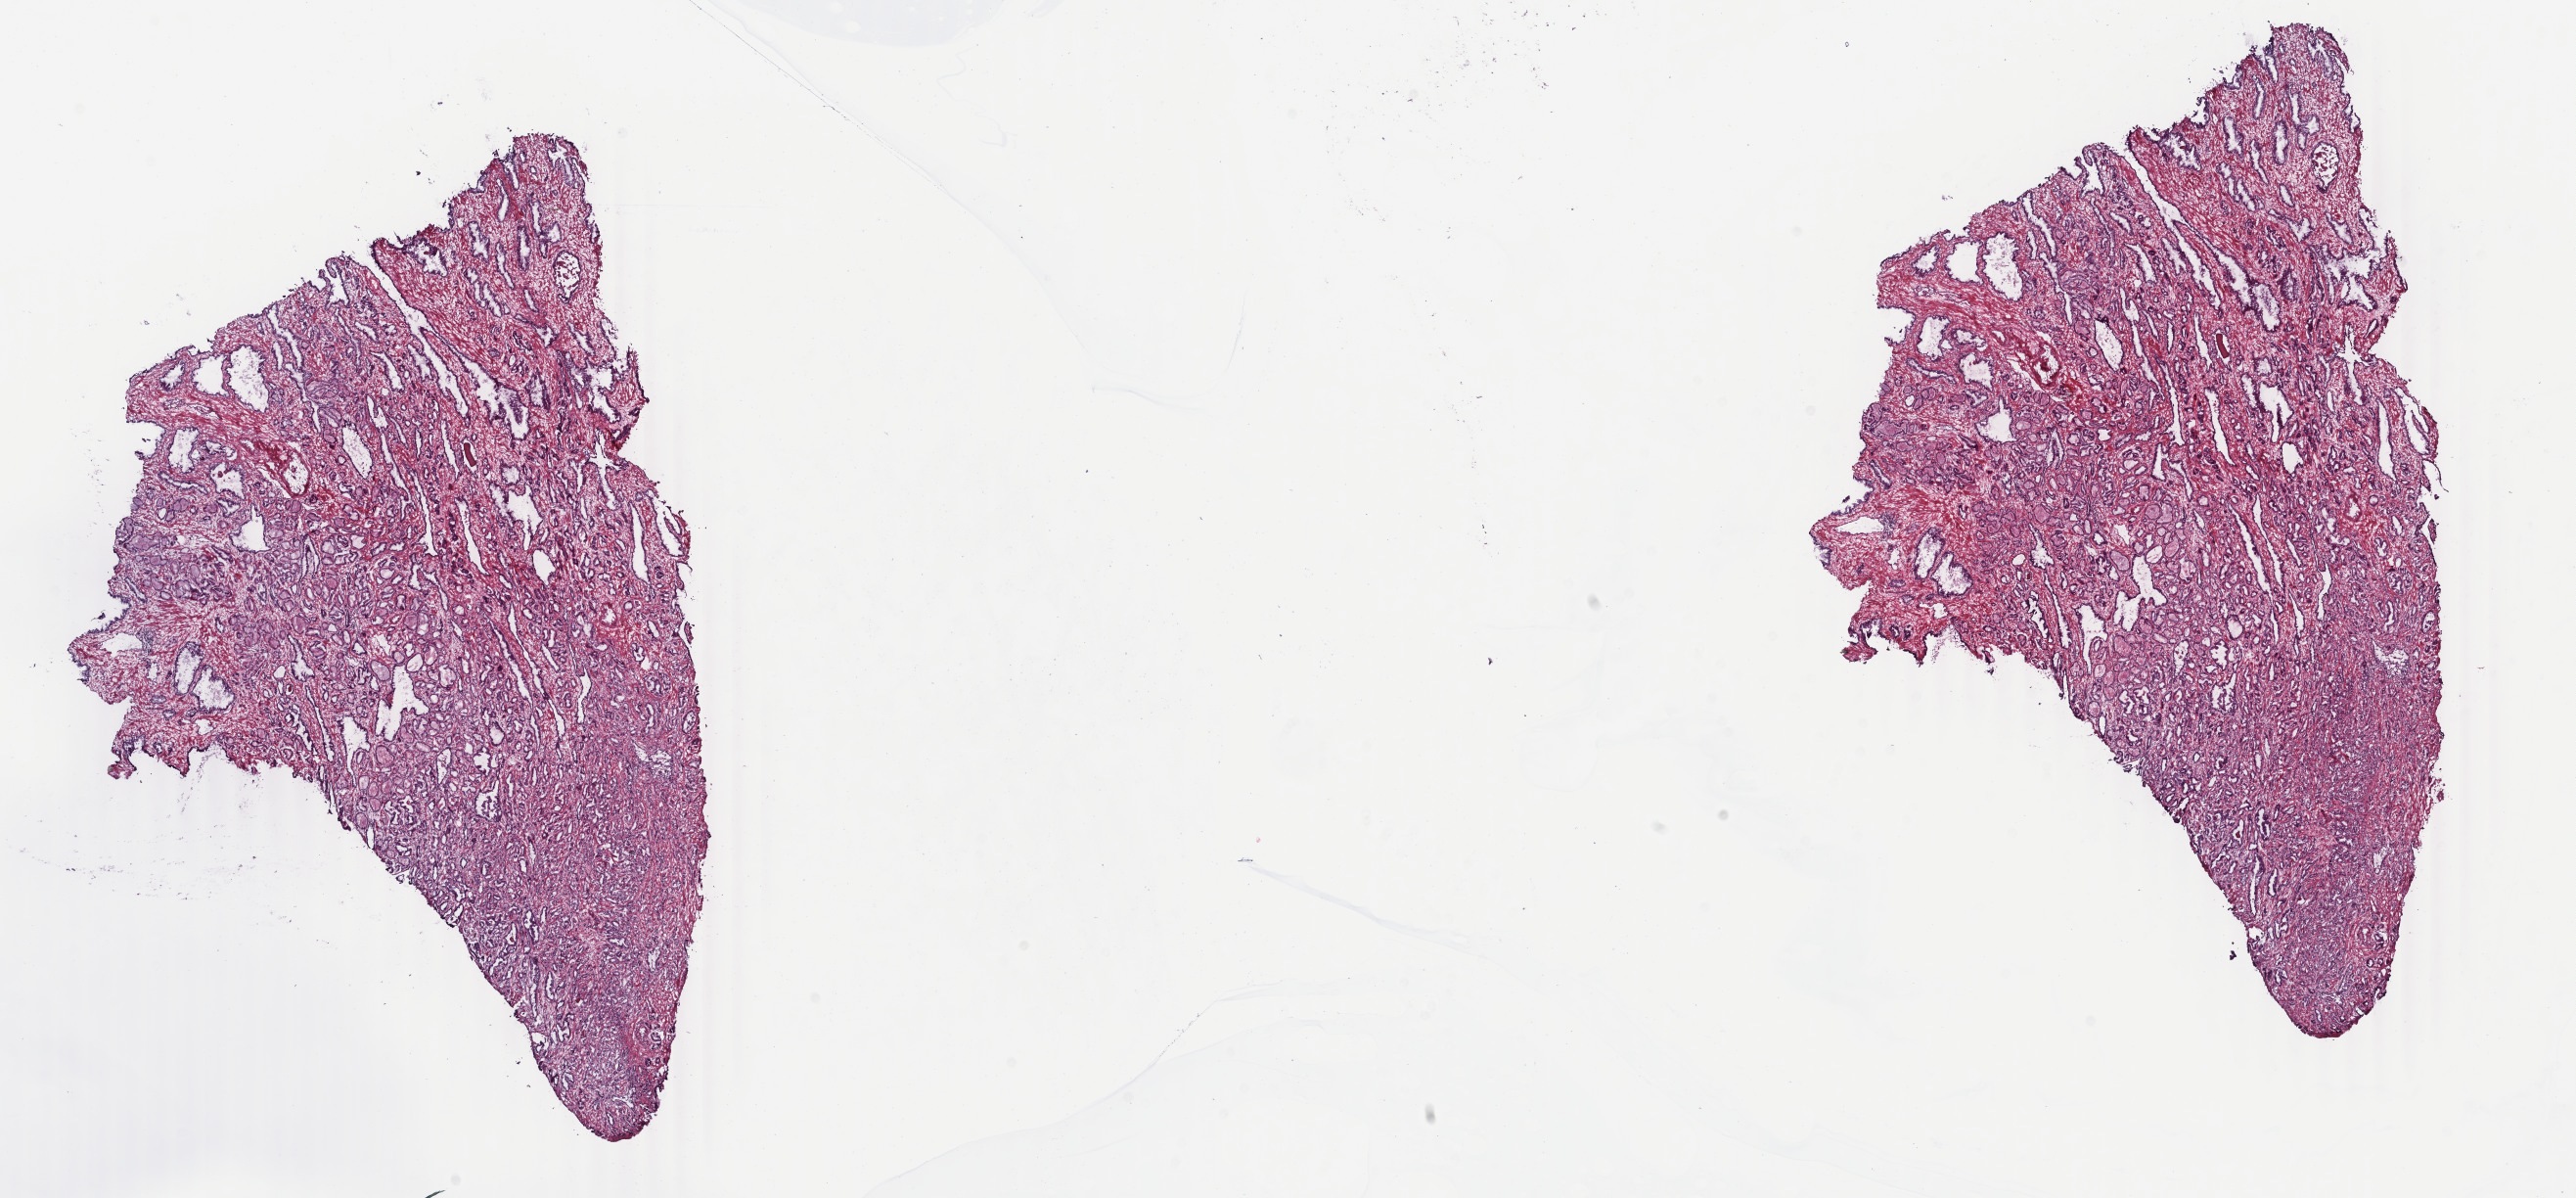
H&E whole-slide image, shown as a low-resolution overview of the whole scanned area (about 20.9 x 9.7 mm), frozen section from the top of the tissue portion, sample: primary tumour, prostate. Male, age 60 years at initial diagnosis. Gleason score: 7 (3+4). Composition of this section per pathologist review: tumour cells 70%, tumour nuclei 80%, normal cells 0%, stromal cells 30%, necrosis 0%. Infiltration values recorded for this section: lymphocyte infiltration 0%, monocyte infiltration 0%, neutrophil infiltration 0%.
Pathologic diagnosis: Adenocarcinoma, NOS (prostate gland). Laterality: bilateral.